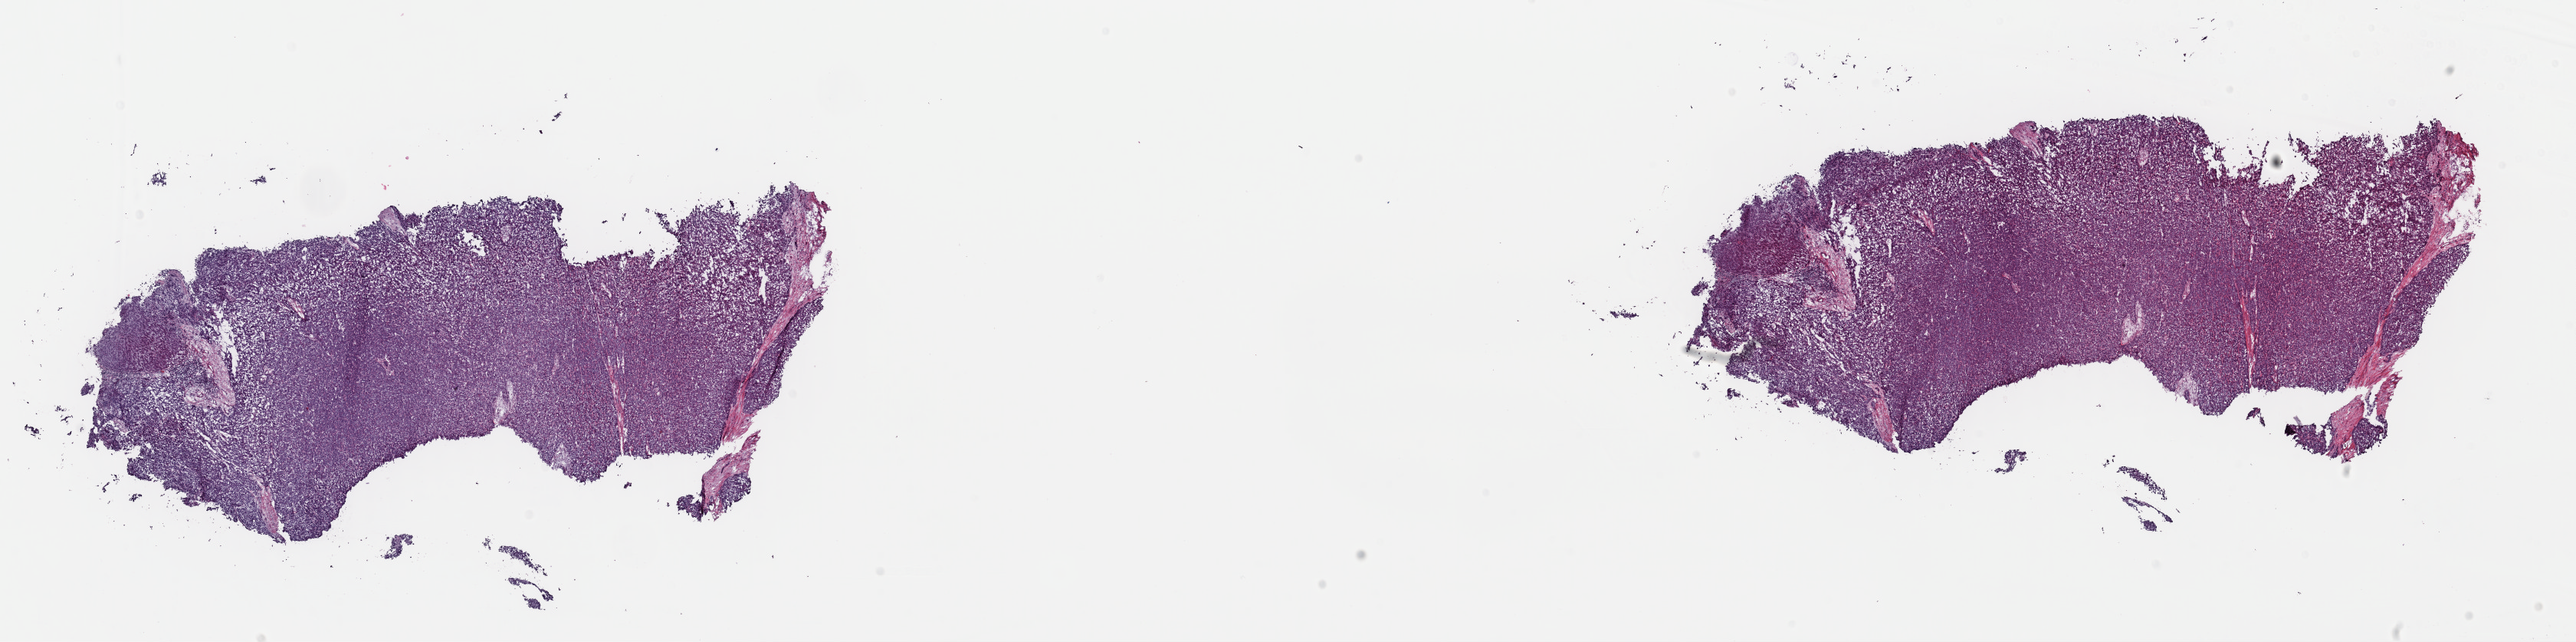
Whole-slide histology image, Hematoxylin and eosin (H&E) stained, low-resolution overview of the scanned area, about 26.5 x 6.6 mm, frozen section from the top of the tissue portion, liver, primary tumour sample. Male, age 61 years at initial diagnosis. Composition of this section per pathologist review: tumour cells 85%, tumour nuclei 85%.
Diagnosis: Hepatocellular carcinoma, NOS.